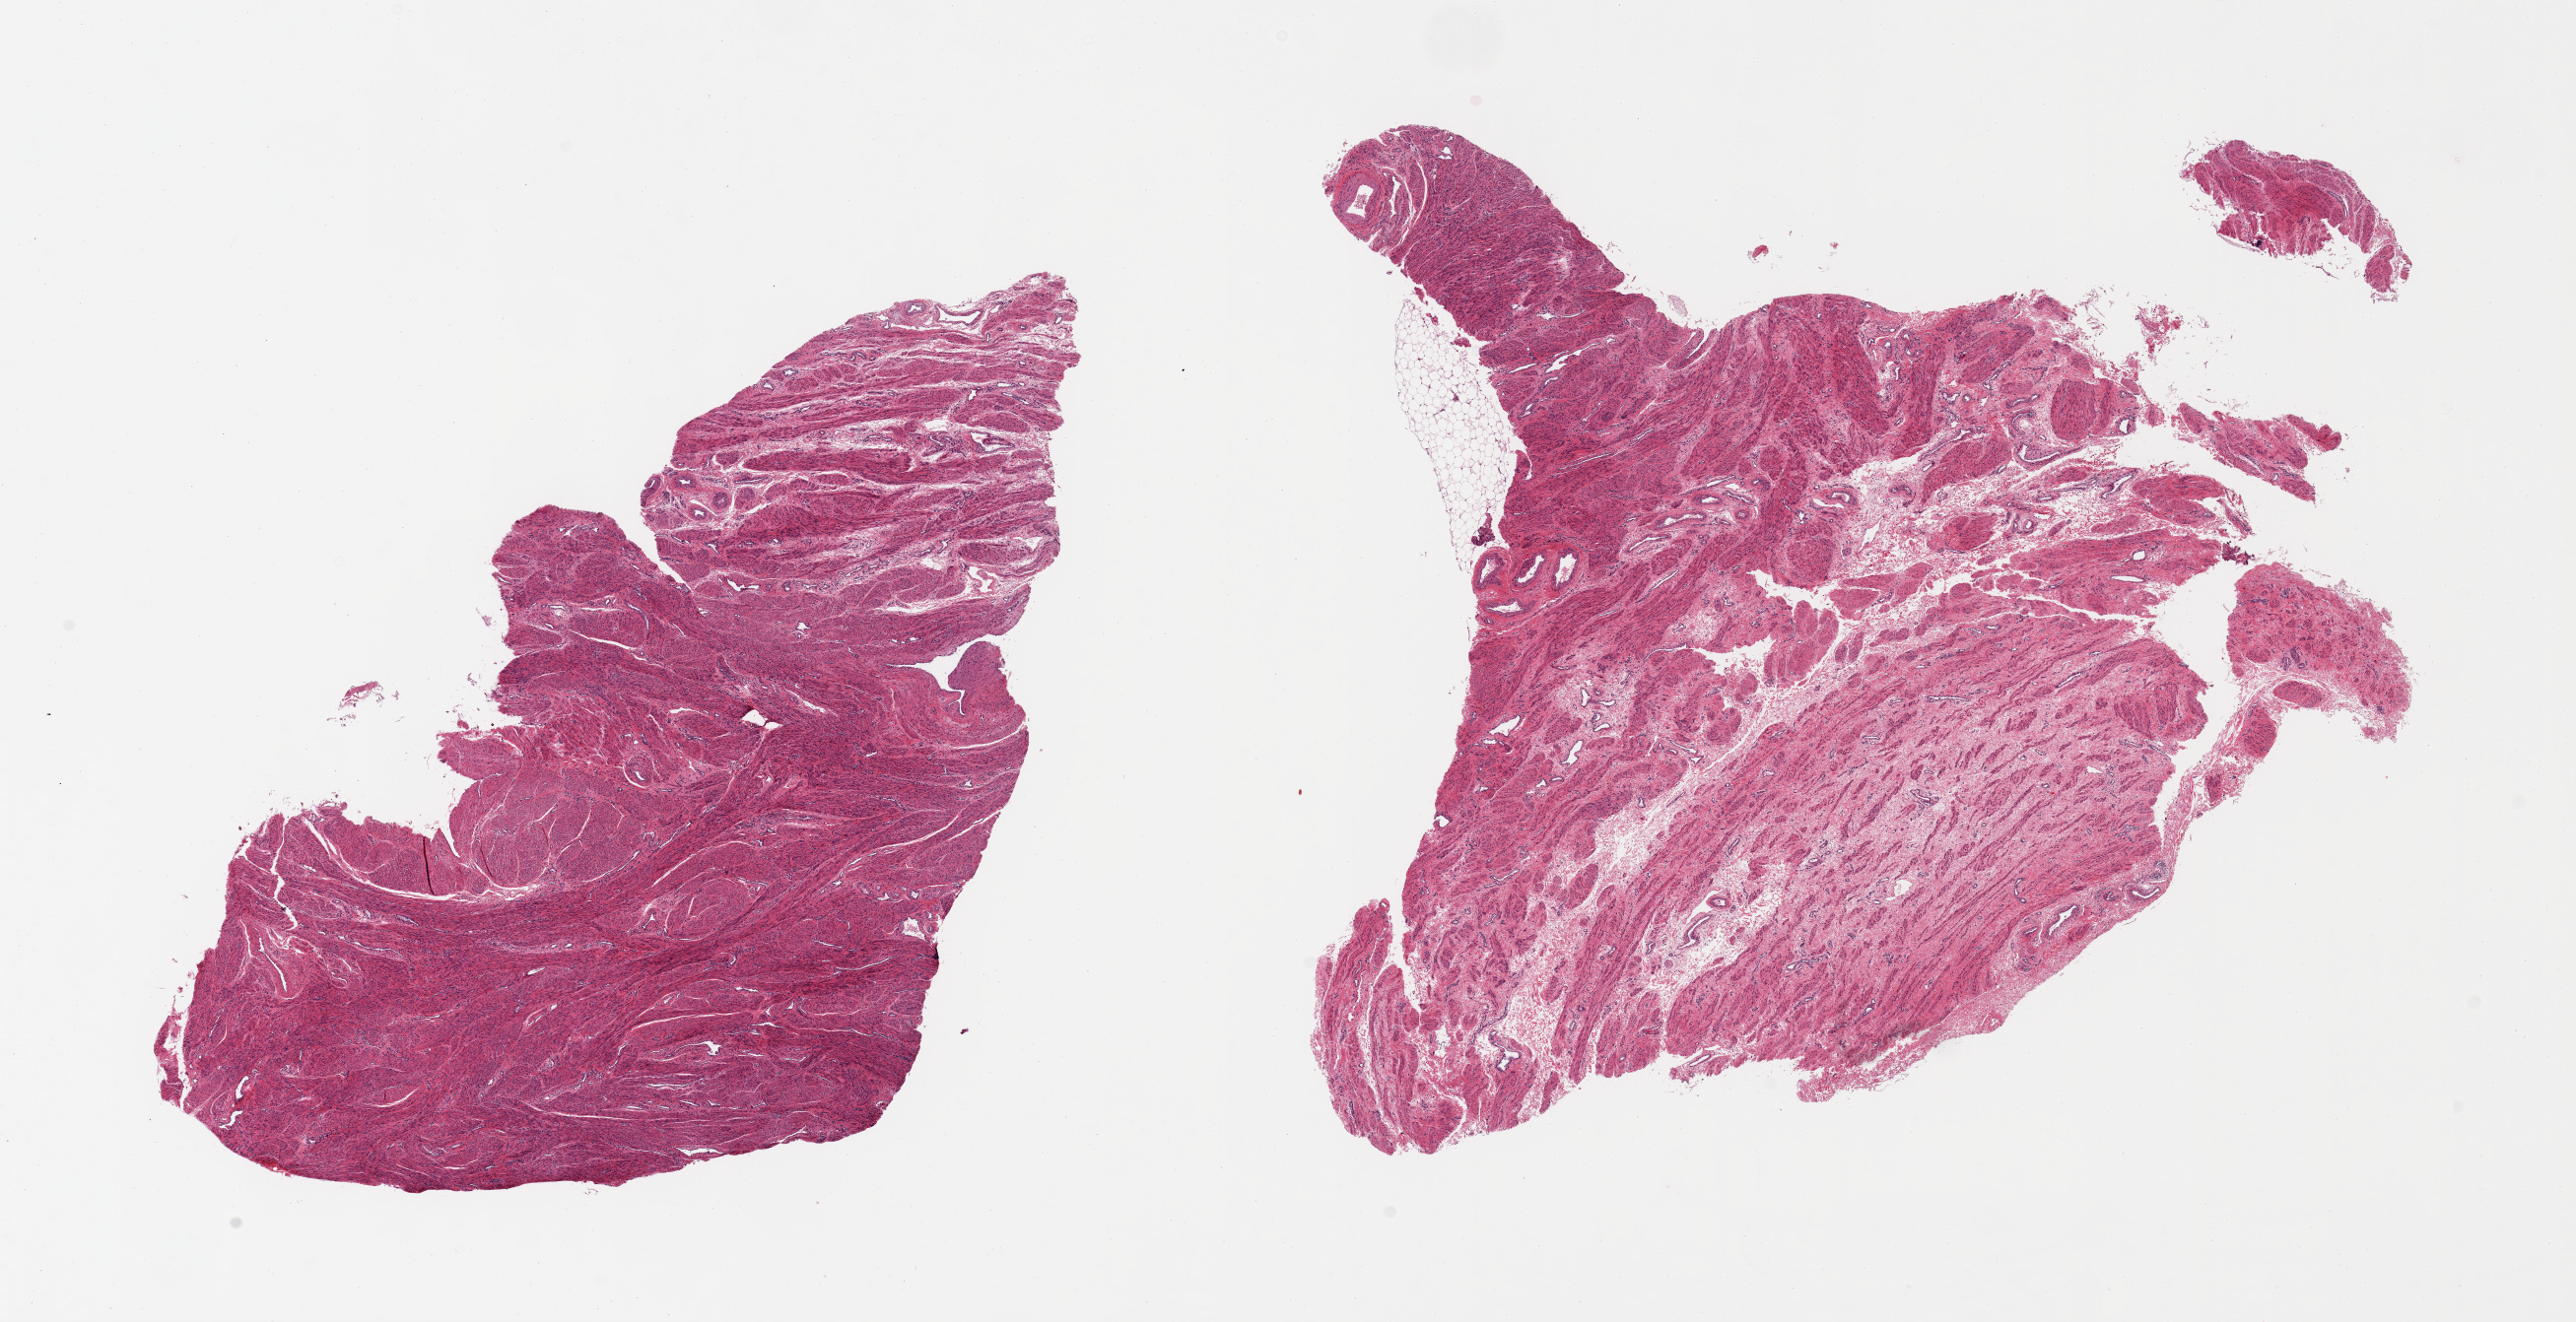
Haematoxylin and eosin whole-slide image — whole scanned area (about 20.7 x 10.6 mm, slide scanned at 20x) shown as a low-resolution overview. PAXgene-fixed, paraffin-embedded tissue. Target tissue: uterus. Donor tissue sample.
Review note (as recorded): 2 pieces, myometrium, no endoemetrium.